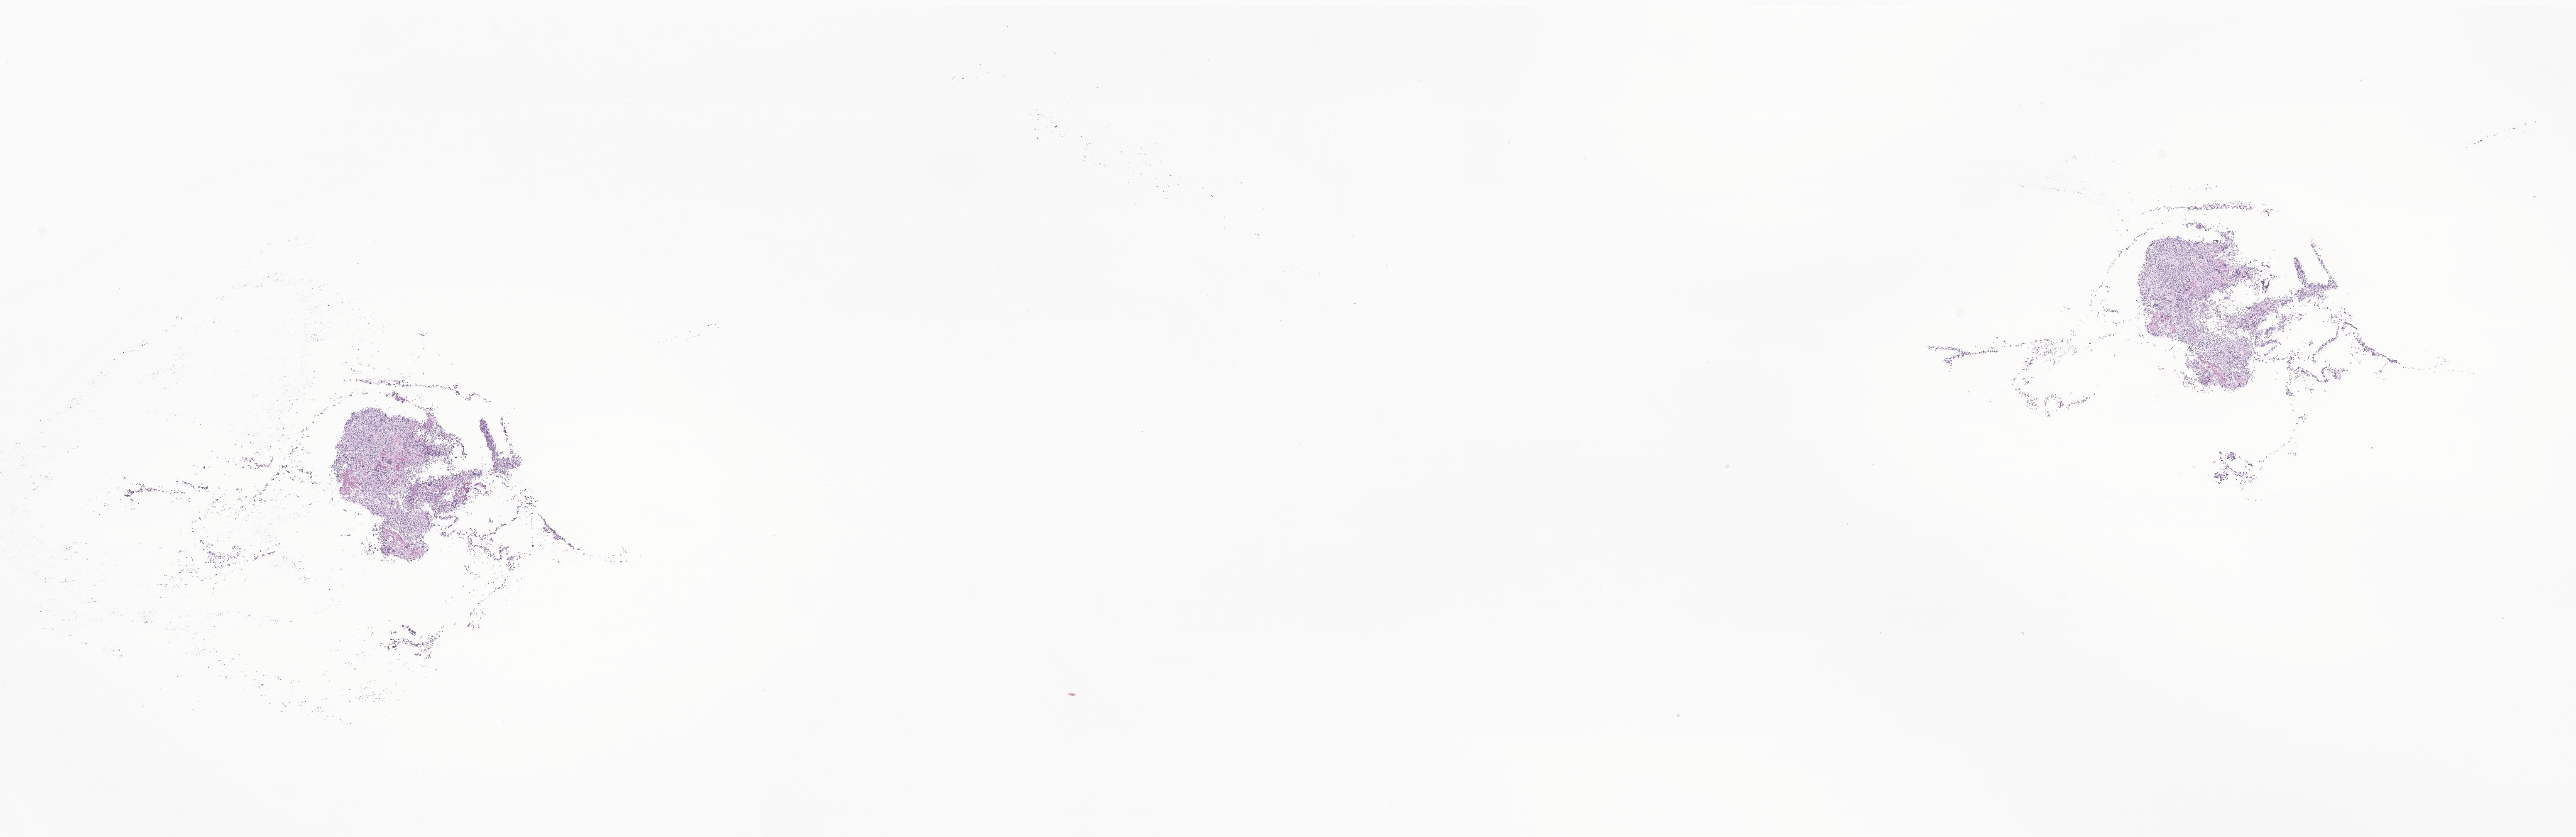
Digitized haematoxylin and eosin-stained section of tumor tissue from the brain stem — low-resolution overview of the scanned area, about 26.2 x 8.5 mm; frozen section (OCT-embedded). Female patient, age 144 months (12 years).
Diagnosis: Medulloblastoma, NOS.